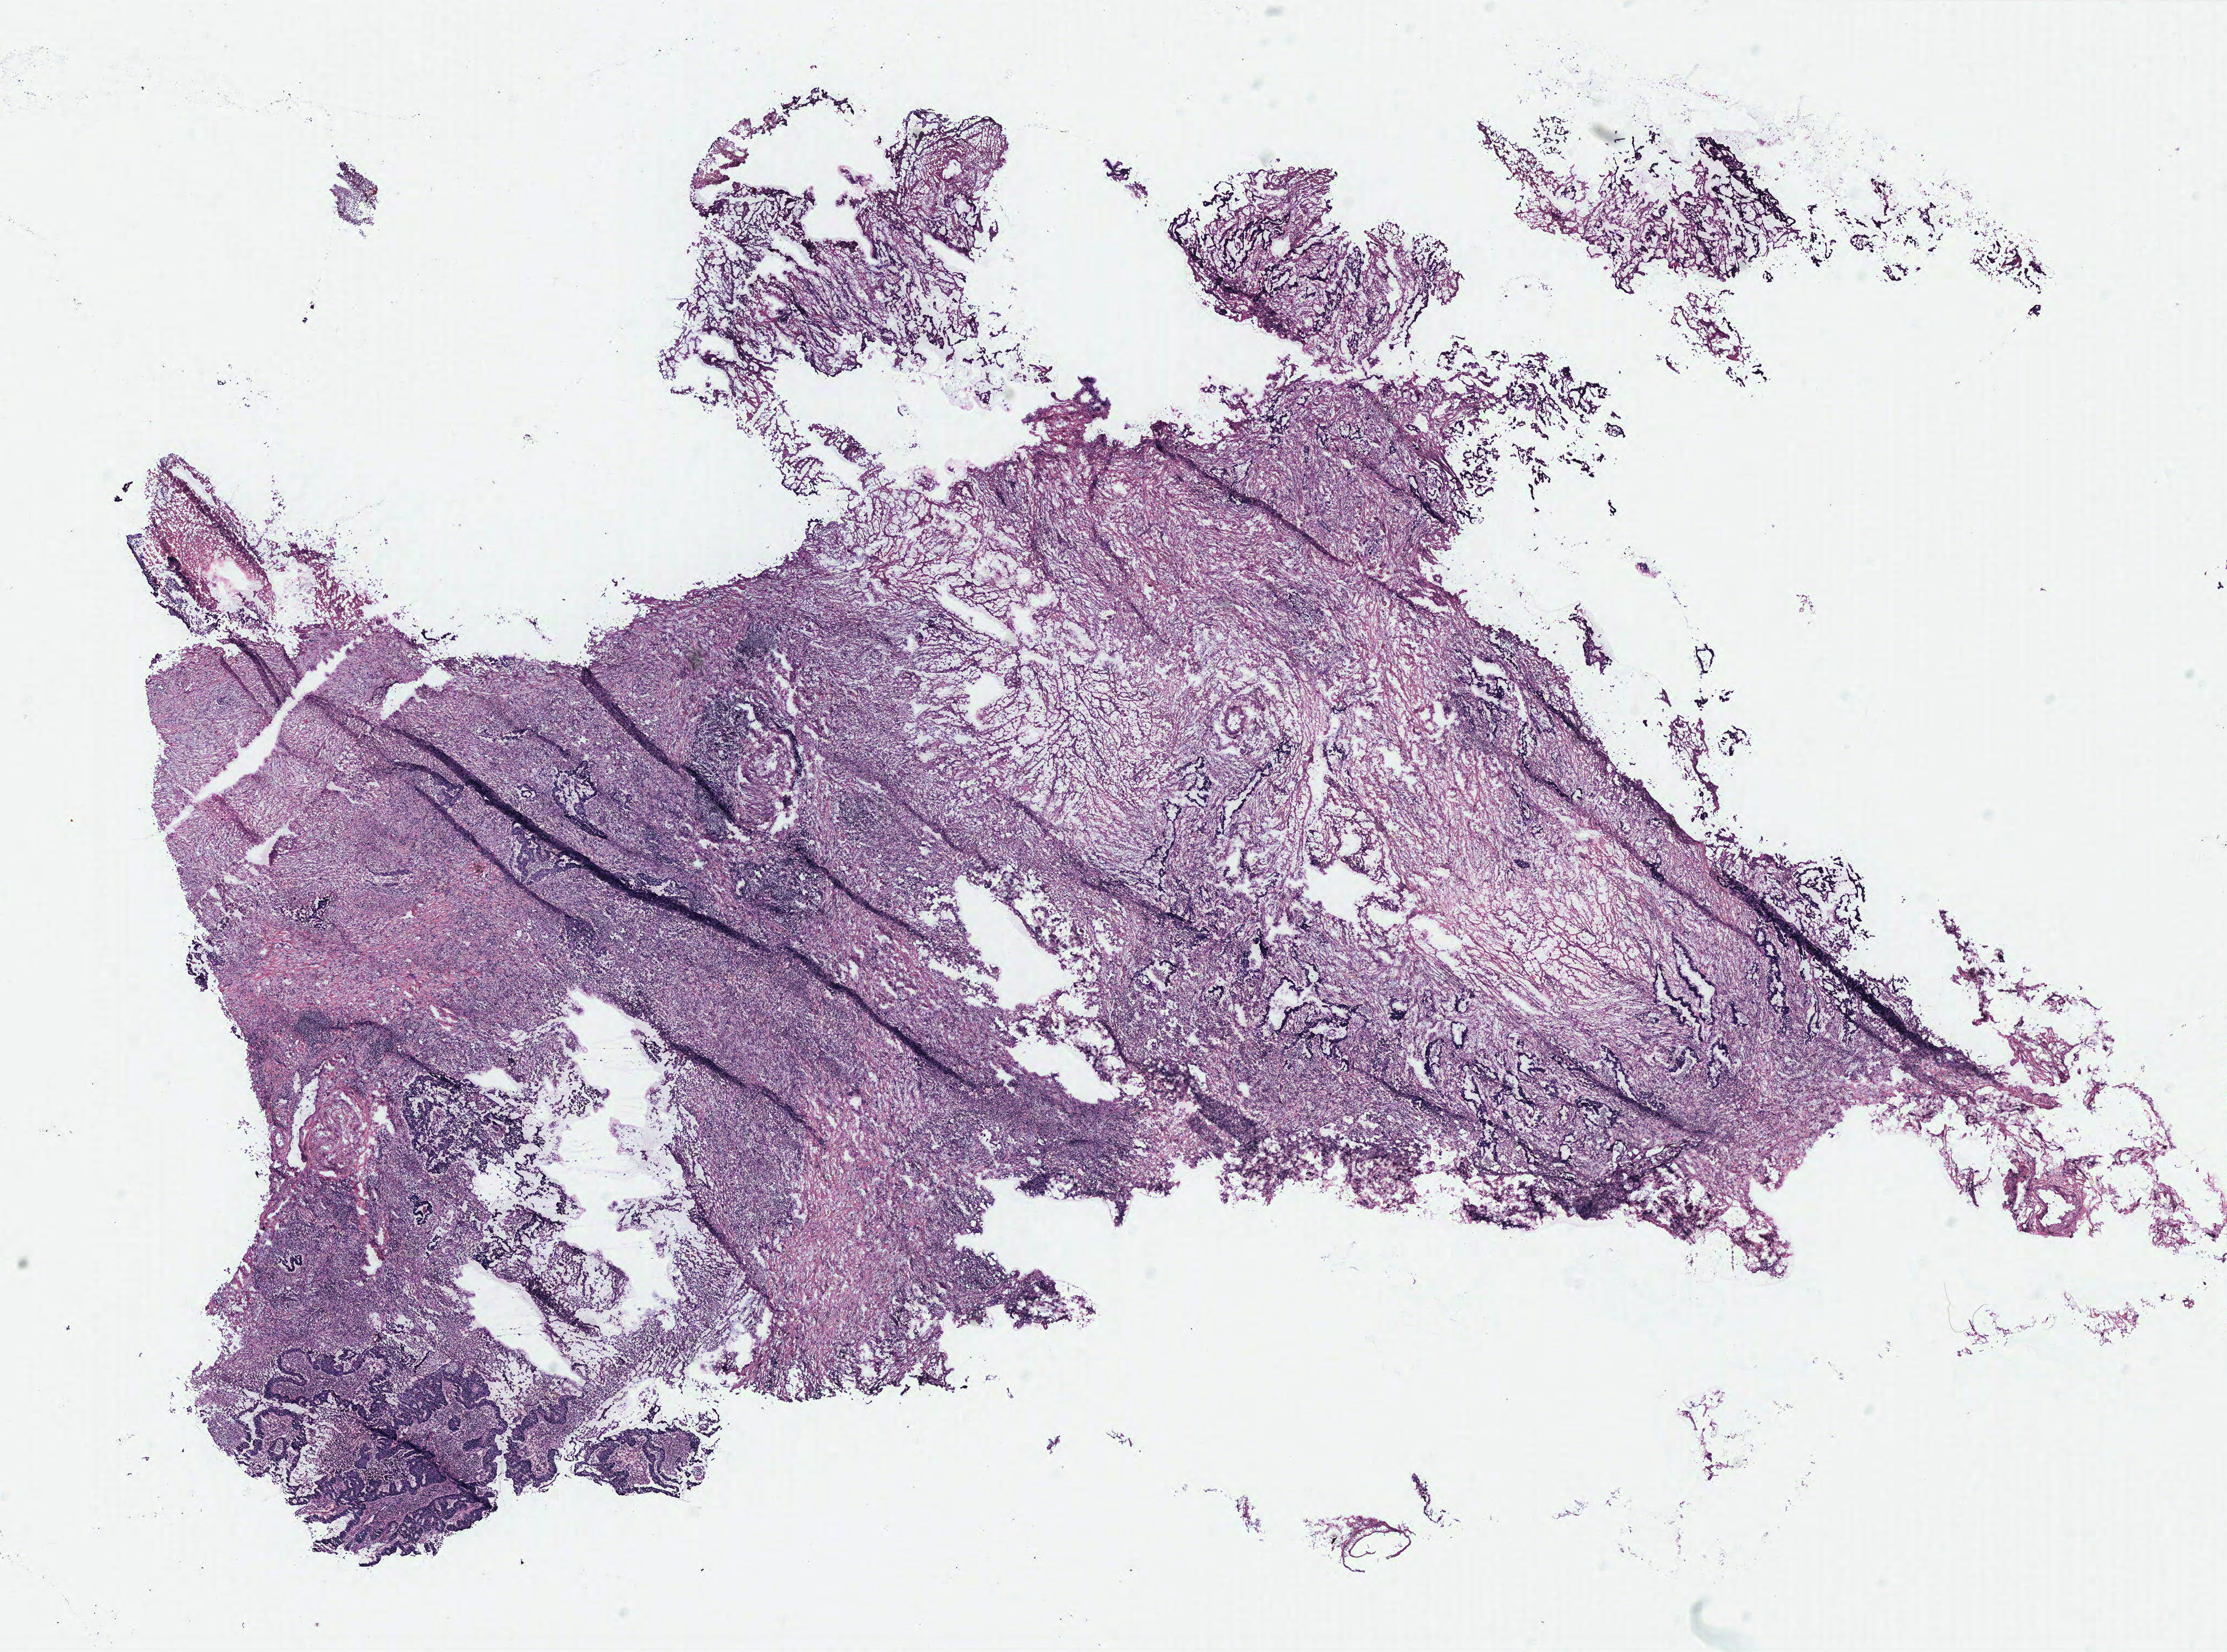
Digitized H&E-stained tissue section (whole slide), whole scanned area (about 16.3 x 12.1 mm) shown as a low-resolution overview. Colon, tissue type not recorded.
* patient diagnosis (cohort enrolment): colon cancer (colon)